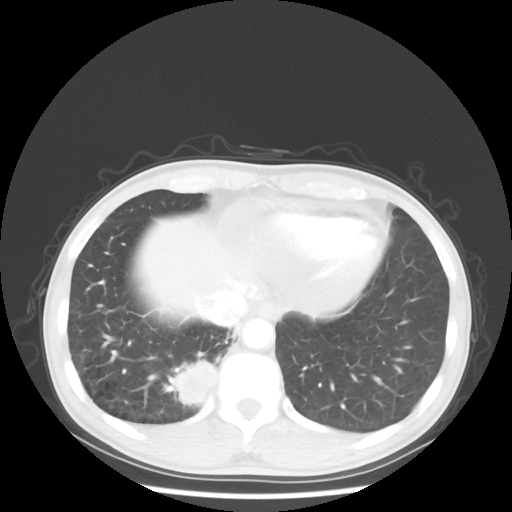
Chest CT, one axial slice. Slice 10 of 58 in the series (ordered by position). 100 kVp. Lung window (W 1500 / L -600 HU). 512 × 512 image matrix, field of view 360 × 360 mm. Male patient, age 56 years. From the clinical record (not read from this slice): clinical TNM (as recorded): T2 N1 M1.
Annotated regions visible in this slice (bounding box drawn by a radiologist):
- lung tumour (recorded histology: adenocarcinoma): bounding box [x1, y1, x2, y2] px = [165, 359, 219, 409]